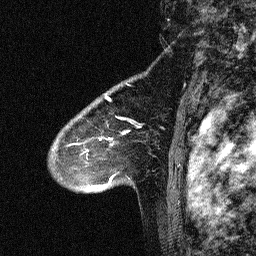
Breast MRI (dynamic contrast-enhanced), one sagittal slice. Slice 46 of 64 in the series (ordered by position). Dynamic contrast-enhanced study with each time point stored as its own series, time point 2 of 3 at this slice position (early post-contrast, ordered by acquisition time). 1.5 T. TE 4.5 ms, TR 11 ms. 256 × 256 image matrix. Female patient, age 46 years. Case-level facts recorded for this patient, not image findings: setting: breast cancer imaged before/during neoadjuvant chemotherapy; receptor status: HER2-positive.
Structures marked on this image (semi-automatic segmentation, software-assisted and operator-edited):
- analysis volume of interest (the breast-tissue region the enhancement analysis was run in; not a lesion): bounding box <42,80,150,180> (left, top, right, bottom; pixels)
- tumour enhancement mask (voxels above the 90 % enhancement threshold inside the analysis volume of interest): <65,97,143,148>